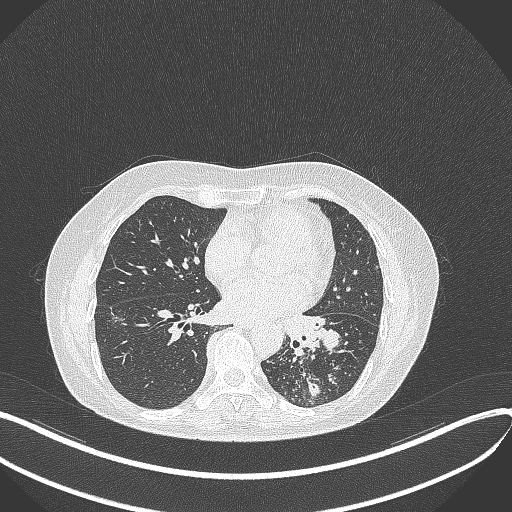
Chest CT, one axial slice; slice 178 of 429 in the series (ordered by position); reconstruction kernel B70f; 100 kVp; lung window (W 1500 / L -600 HU); 1 mm slice thickness; 512 × 512 image matrix, field of view 400 × 400 mm. Female patient, age 63 years. Case-level facts recorded for this patient, not image findings: clinical TNM (as recorded): T1b N0 M0; histopathological grade: G2-3.
Annotated regions visible in this slice (bounding box drawn by a radiologist):
- lung tumour (recorded histology: adenocarcinoma): bounding box <279,313,339,358> (left, top, right, bottom; pixels)